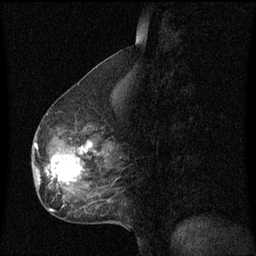
Breast MRI (dynamic contrast-enhanced), one sagittal slice. Slice 30 of 60 in the series (ordered by position). Dynamic contrast-enhanced series, image 2 of 3 at this slice position (ordered by acquisition). 1.5 T. TE 4.2 ms, TR 8.4 ms. 2 mm slice thickness. 256 × 256 image matrix, field of view 200 × 200 mm. Patient: female, 49 years. From the clinical record (not read from this slice): setting: breast cancer imaged before/during neoadjuvant chemotherapy; receptor status: HR-positive, HER2-negative.
Structures marked on this image (semi-automatically segmented with operator editing):
- analysis volume of interest (the breast-tissue region the enhancement analysis was run in; not a lesion): box from (x=33, y=126) to (x=116, y=201) px
- tumour enhancement mask (voxels above the 70 % enhancement threshold inside the analysis volume of interest): (x=46, y=142)–(x=94, y=187)